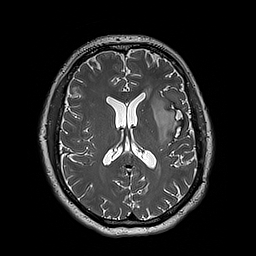
Brain MRI from a brain-tumour surgery series, one axial slice; slice 92 of 192 in the series (ordered by position); 256 × 256 image matrix, field of view 250 × 250 mm. From the clinical record (not read from this slice): histopathology: Astrocytoma; WHO grade: 3.
Outlined on this slice (outlined manually by an expert reader):
- tumour: bounding box (x1, y1, x2, y2) in pixels: (152, 94, 179, 144)